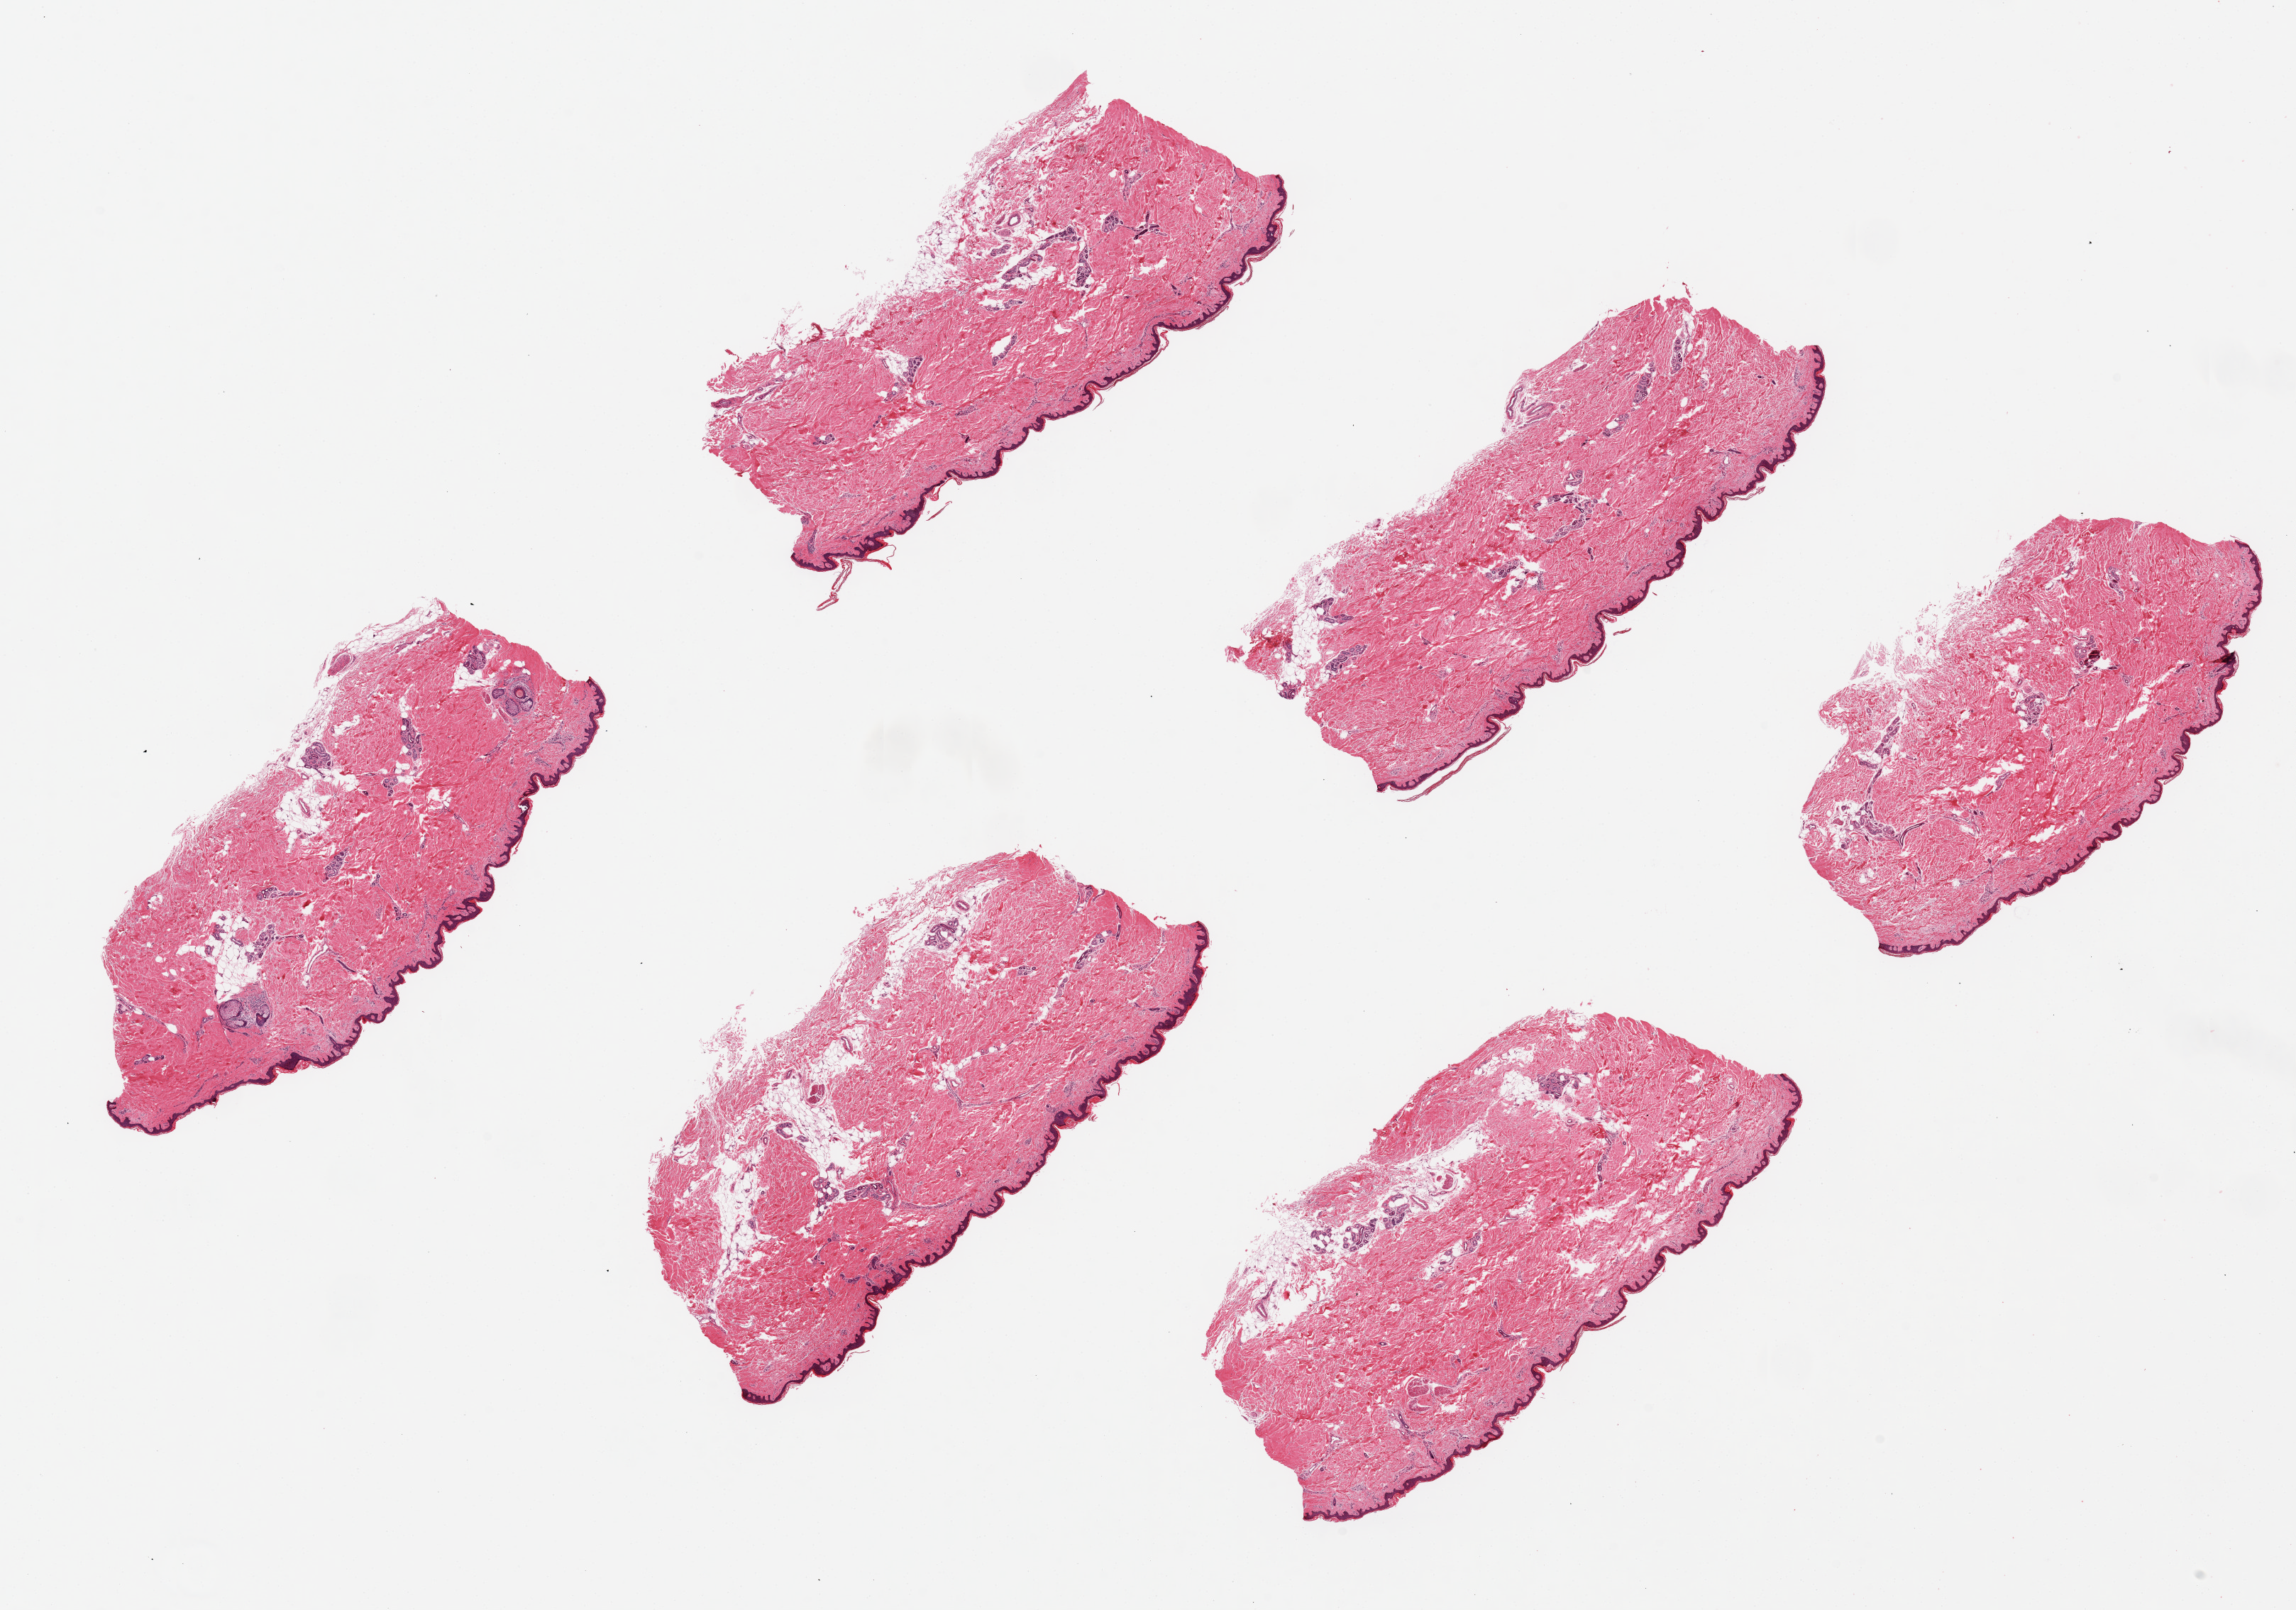
Hematoxylin and eosin (H&E) whole-slide image, brightfield — shown as a low-resolution overview of the whole scanned area (about 25.6 x 17.9 mm, slide scanned at 20x); PAXgene-fixed paraffin-embedded (PFPE) section; sampled site (target tissue): skin of lower leg; tissue donor sample. Male donor.
Reviewer comment on this tissue sample: 6 pieces, ~7x3mm. Squamous mucosa is ~2-3% of thickness.